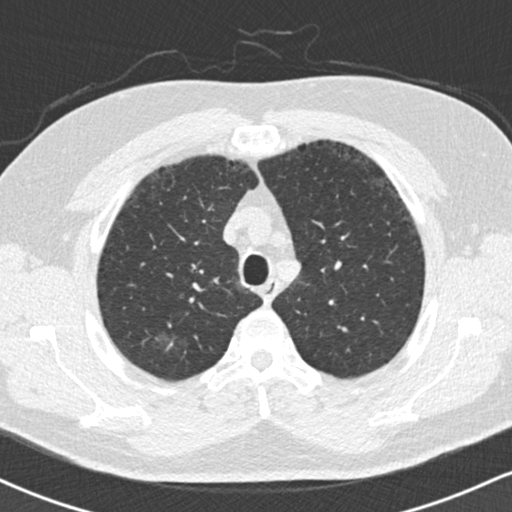
Low-dose screening chest CT, one axial slice. Reconstruction kernel B30f. Lung window (W 1500 / L -600 HU). 2 mm slice thickness. 512 × 512 image matrix, field of view 320 × 320 mm.
Annotated regions visible in this slice (outlined manually by an expert reader):
- lesion 1 (tumor, upper lobe of right lung): bounding box (x1, y1, x2, y2) in pixels: (156, 331, 178, 353)